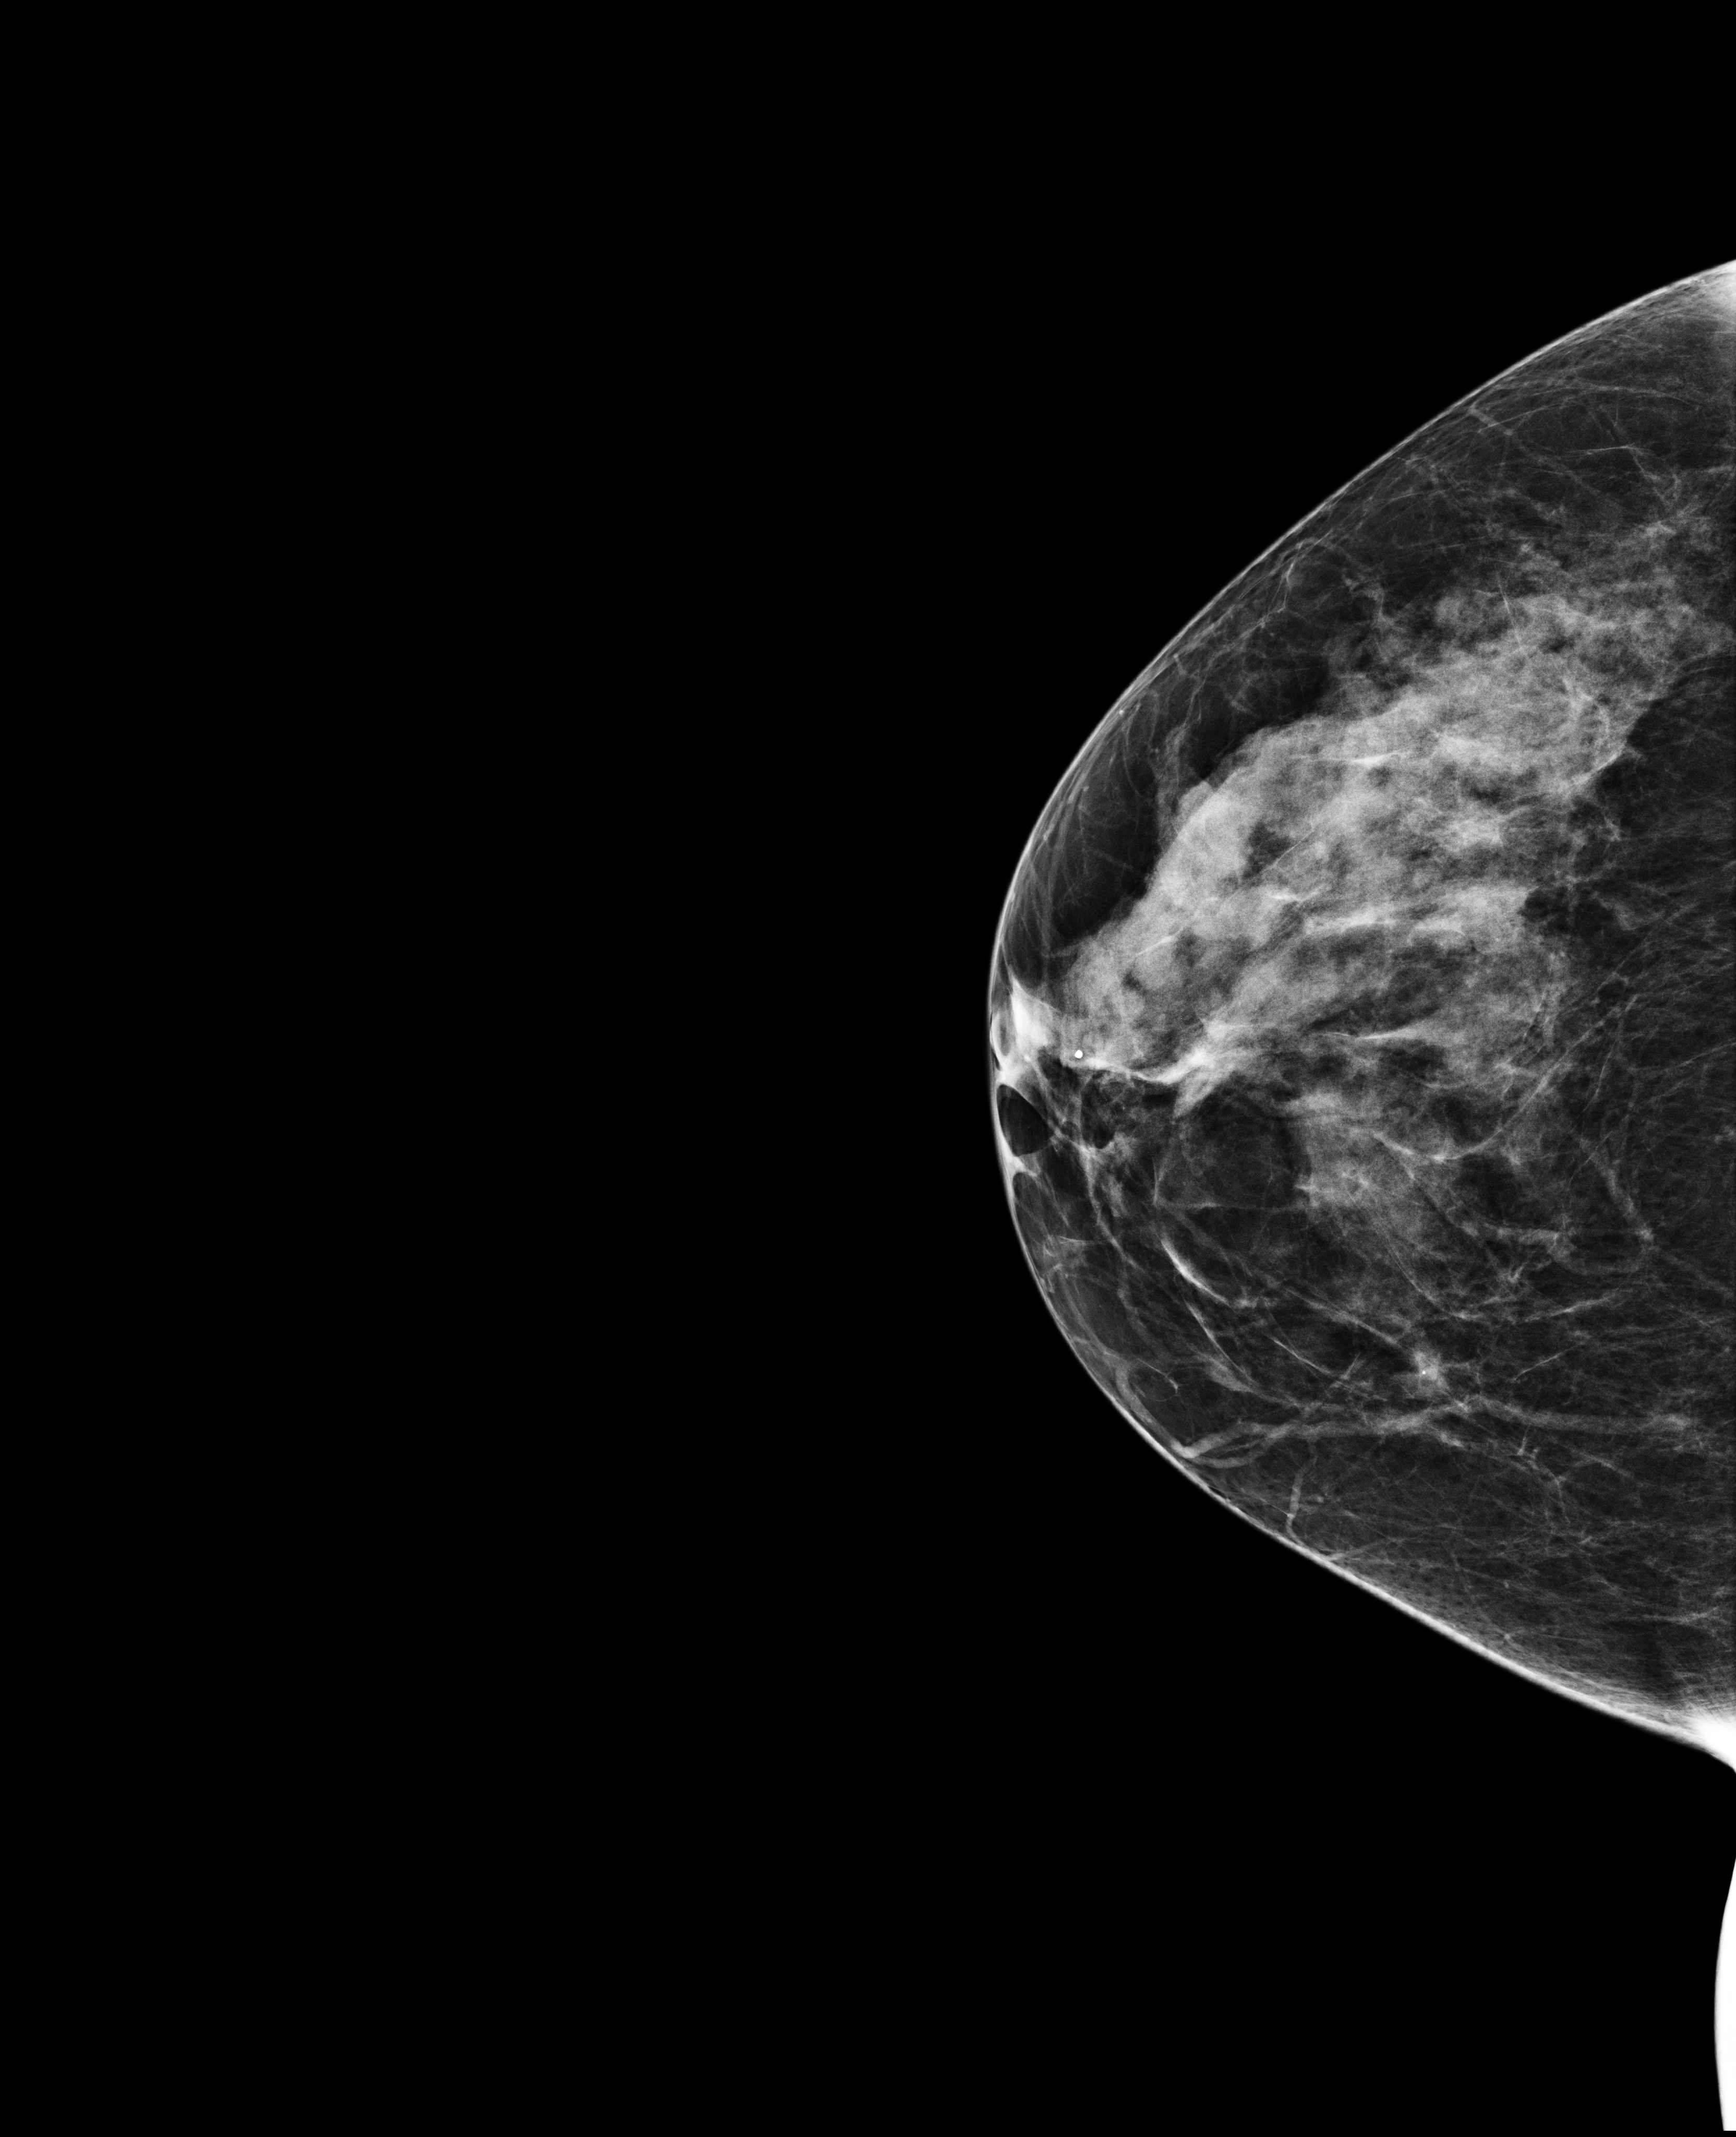
Digital mammogram (FFDM); right breast; craniocaudal (CC) view; screening examination. Patient: female, 48 years.
BI-RADS breast density category at the screening exam (both breasts, scale 1–4): 3. Final BI-RADS category for the screening round (tomosynthesis exam, both breasts): category 1. Recall: no recall after this screen.